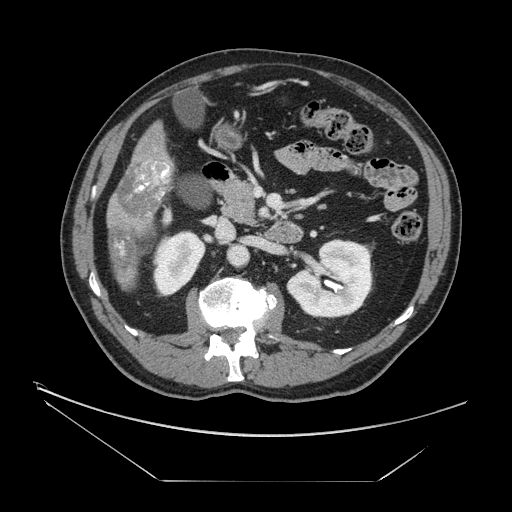
Contrast-enhanced abdominal CT, one axial slice; position 61 of 161 along the scan axis; 120 kVp; intravenous contrast given; soft-tissue window (W 400 / L 40 HU); 2.5 mm slice thickness; 512 × 512 image matrix, field of view 440 × 440 mm. Male patient, age 65 years. Case-level facts recorded for this patient, not image findings: diagnosis: colorectal cancer liver metastases, imaged before liver resection; multiple liver metastases: yes.
Structures marked on this image (expert manual segmentation):
- liver: bounding box <108,125,174,290> (left, top, right, bottom; pixels)
- portal vein (with intrahepatic branches): <136,162,170,199>
- liver metastasis: <109,229,139,270>
- liver metastasis: <117,162,172,218>